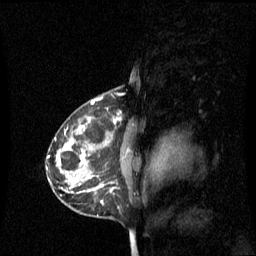
Breast MRI (dynamic contrast-enhanced), one sagittal slice. Dynamic contrast-enhanced series, image 2 of 3 at this slice position (ordered by acquisition). 1.5 T. TE 4.2 ms, TR 8.4 ms. 2.1 mm slice thickness. 256 × 256 image matrix, field of view 240 × 240 mm. Patient: female, 42 years. Case-level facts recorded for this patient, not image findings: setting: breast cancer imaged before/during neoadjuvant chemotherapy; receptor status: HR-positive, HER2-negative.
Annotated regions visible in this slice (semi-automatically segmented with operator editing):
- analysis volume of interest (the breast-tissue region the enhancement analysis was run in; not a lesion): box from (x=68, y=116) to (x=137, y=201) px
- tumour enhancement mask (voxels above the 70 % enhancement threshold inside the analysis volume of interest): (x=80, y=120)–(x=117, y=201)